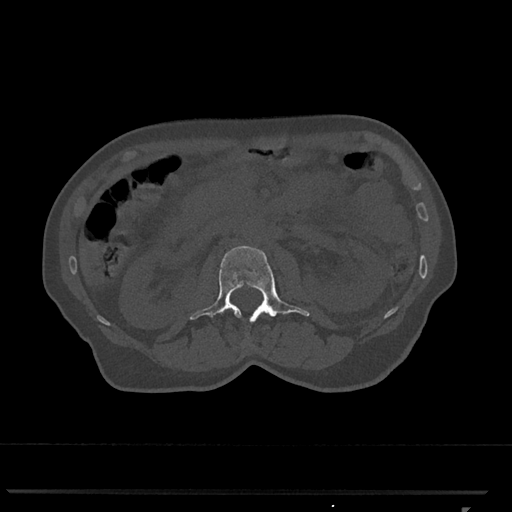
CT including the spine, one axial slice. Slice 346 of 793 in the series (ordered by position). Reconstruction kernel Br40s/3. 120 kVp. Bone window (W 1800 / L 400 HU). 0.5 mm slice thickness. 512 × 512 image matrix. Female patient, age 62 years. Case-level facts recorded for this patient, not image findings: primary cancer: renal.
Annotated regions visible in this slice (semi-automatic segmentation, software-assisted and operator-edited):
- L2 vertebra: bounding box [x1, y1, x2, y2] px = [190, 246, 310, 322]